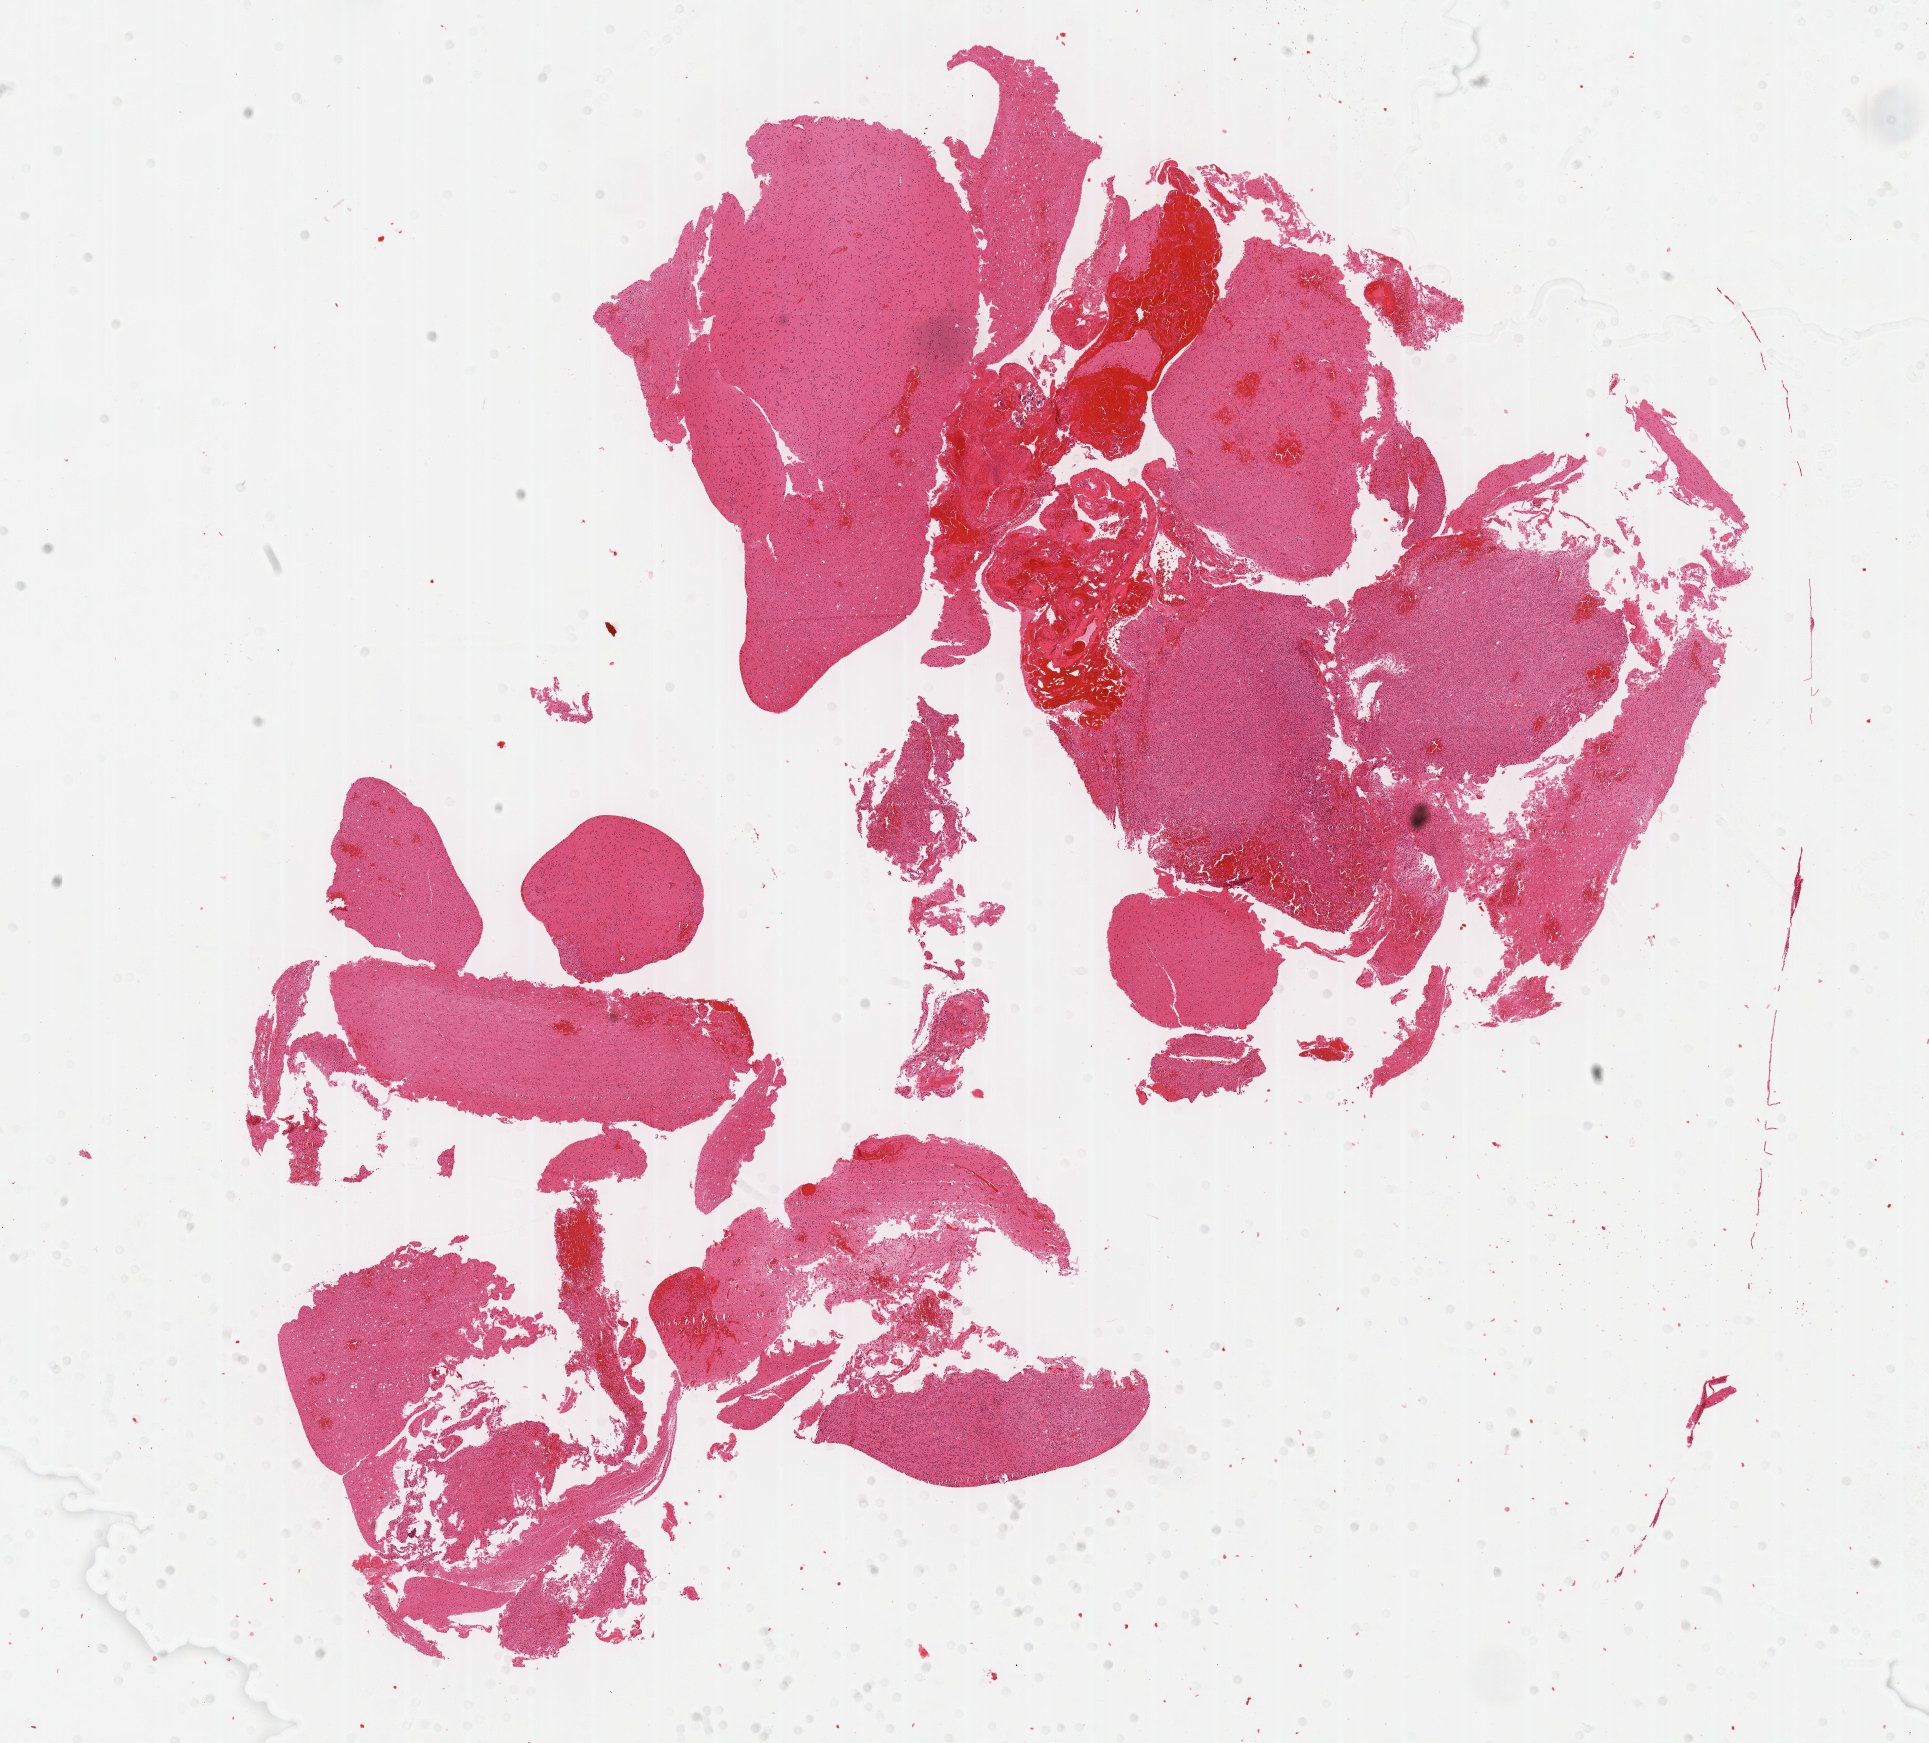
Digitized H&E tissue section (whole slide) — whole scanned area (about 15.6 x 14.1 mm) shown as a low-resolution overview, formalin-fixed paraffin-embedded (FFPE) diagnostic section, primary tumour sample from the brain. Female, age 52 years at initial diagnosis. Histologic grade: G3 (poorly differentiated).
- laterality: left
- diagnosis: Oligodendroglioma, anaplastic (cerebrum)